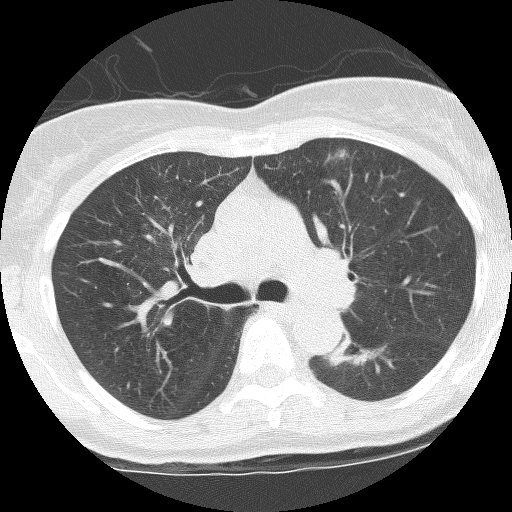
Low-dose screening chest CT, axial slice. Third screening round (two years after baseline). Lung window (W 1500 / L -600 HU). 2.5 mm slice thickness. Lung (sharp) reconstruction kernel (BONE). 120 kVp. 512 × 512 image matrix. Female participant, aged 62 years at enrolment. Former smoker at enrolment.
Expert reader's lesion annotation, bounding box (x1, y1, x2, y2) in pixels: (321, 331, 390, 371). The screening reader recorded 3 non-calcified nodules or masses ≥4 mm on this exam (right upper lobe, left lower lobe, left upper lobe); which of them this box marks is not recorded. Official screen result: positive, other. Later outcome: lung cancer diagnosed 165 days after this screen — squamous cell carcinoma, NOS, left lower lobe, stage IIIB (AJCC 6th edition), 31 mm at pathology.